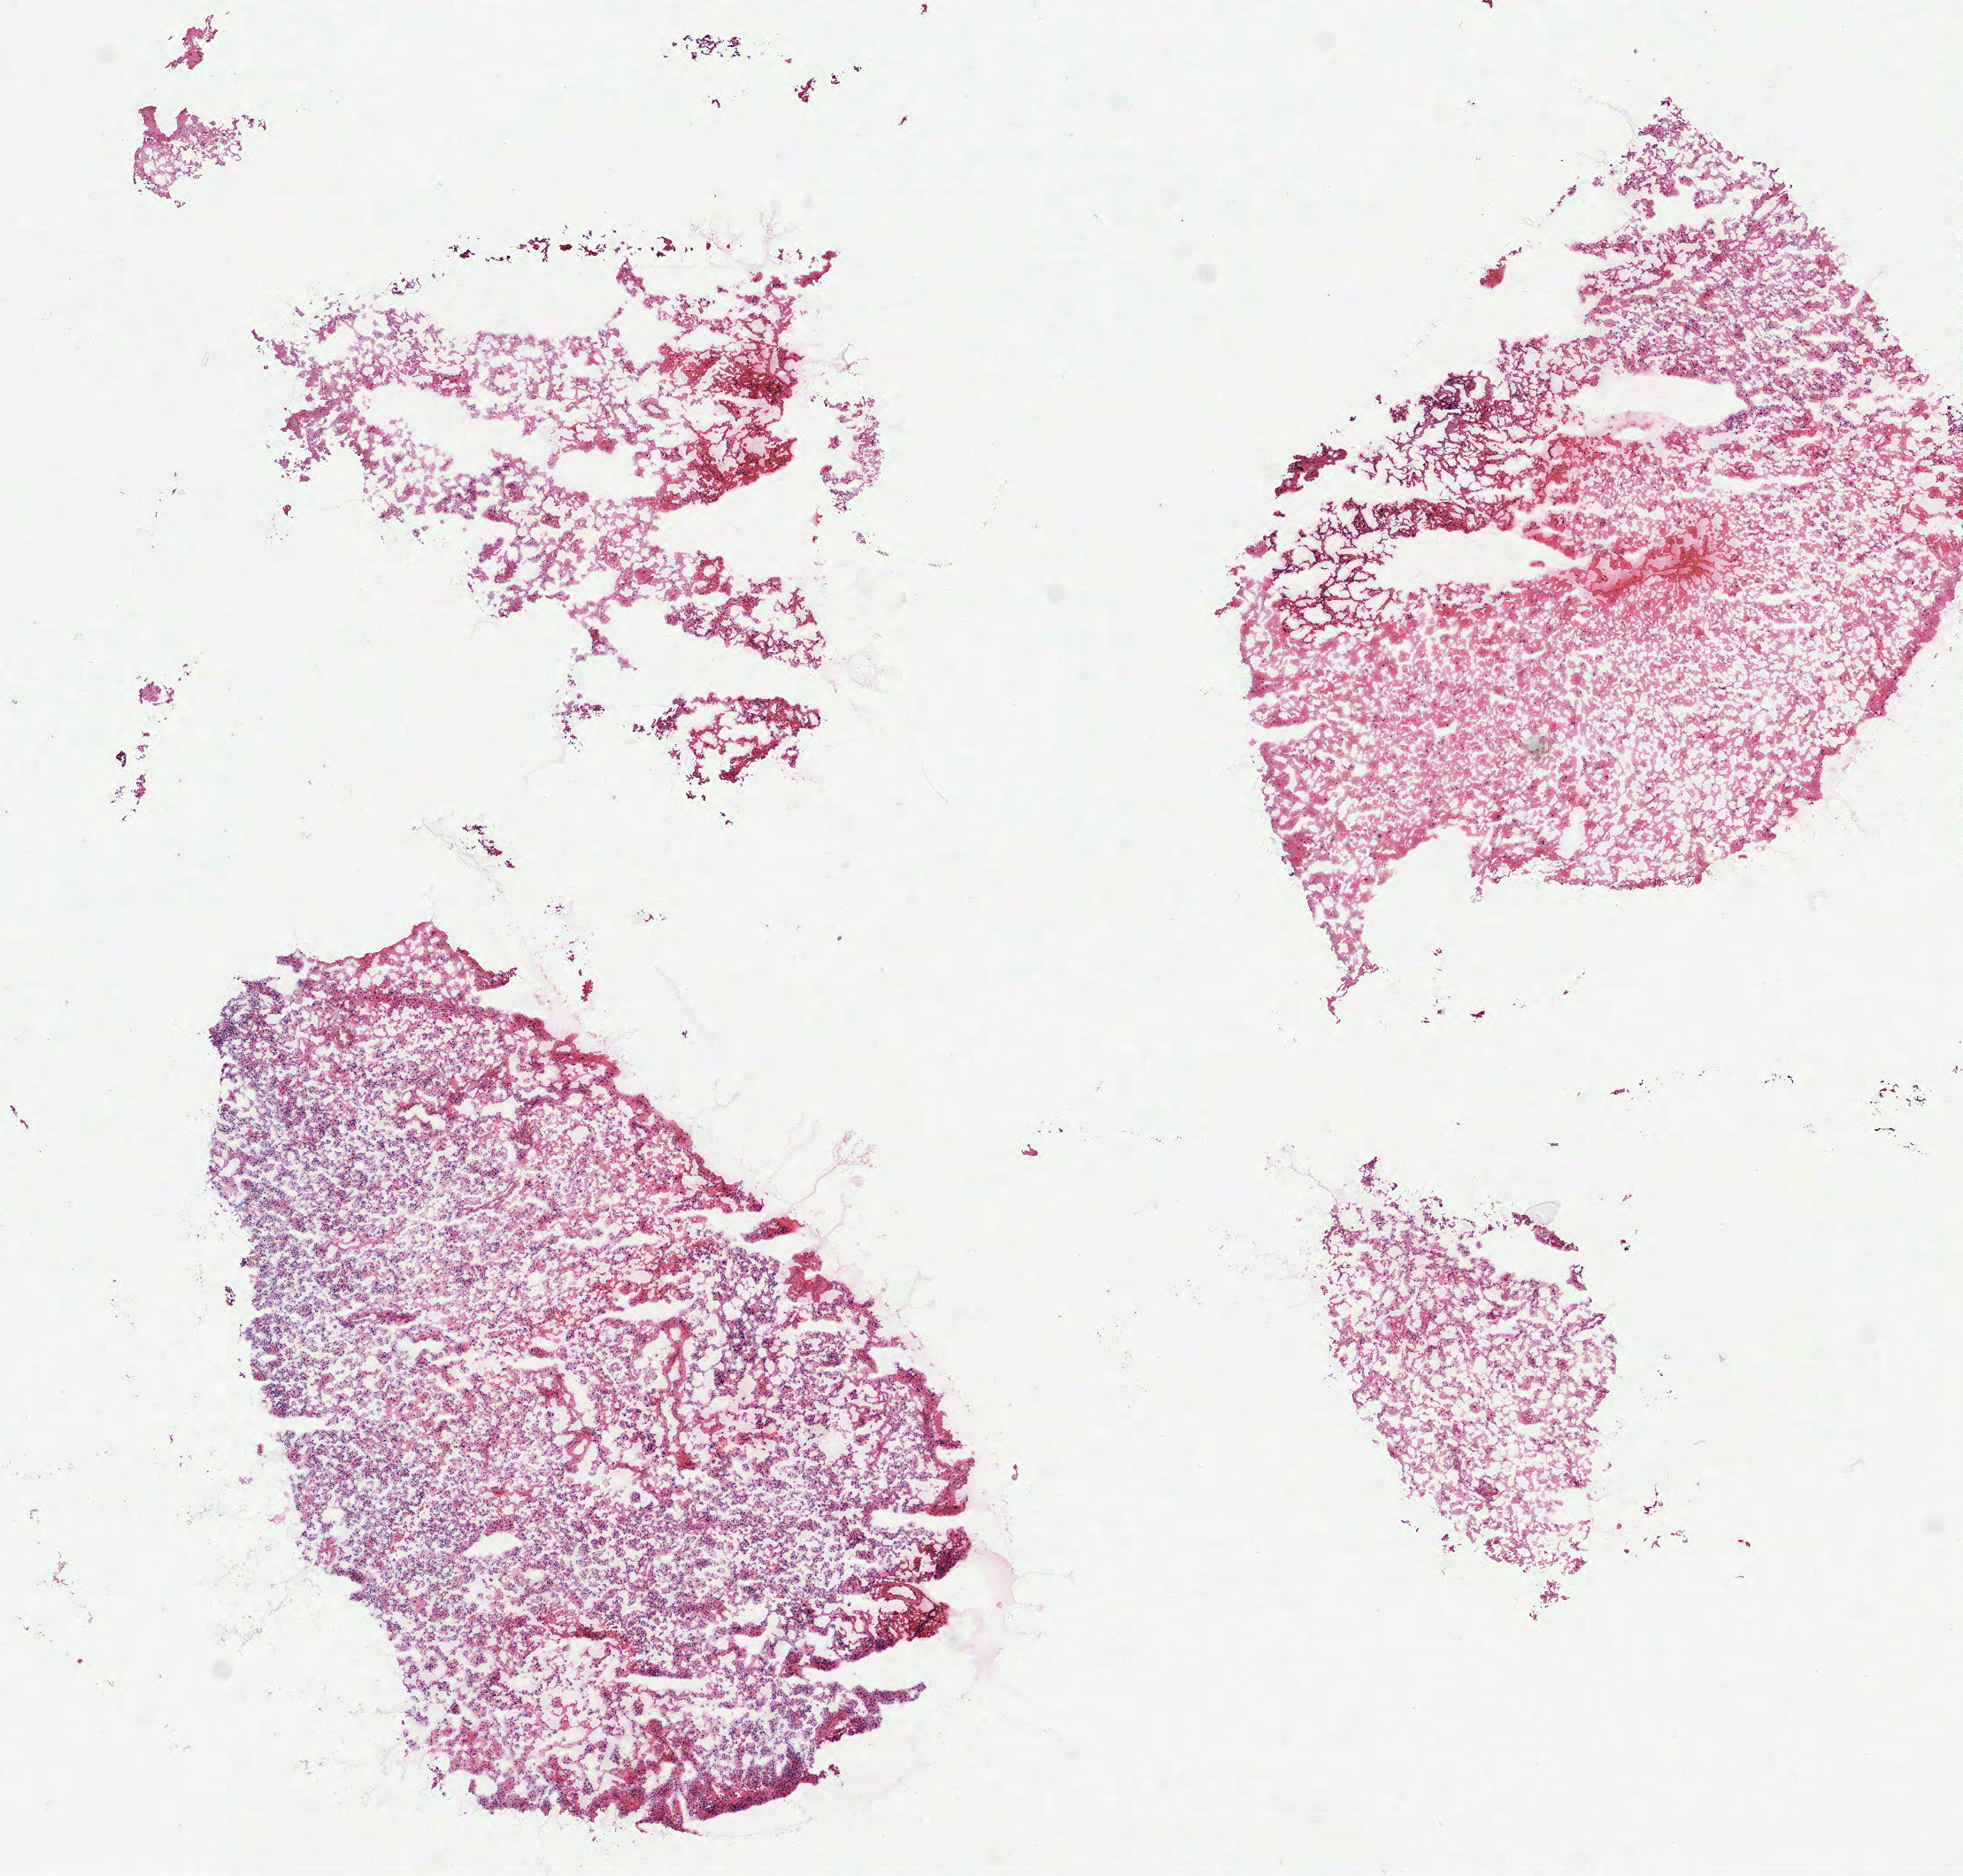
Digitized Hematoxylin and eosin (H&E) stained tissue section (whole slide) — shown as a low-resolution overview of the whole scanned area (about 8.9 x 8.5 mm); frozen section from the top of the tissue portion; brain, primary tumour sample. Male, age 57 years at initial diagnosis. Composition of this section per pathologist review: tumour cells 100%, tumour nuclei 75%, normal cells 0%, stromal cells 0%, necrosis 0%.
Pathologic diagnosis: Glioblastoma.